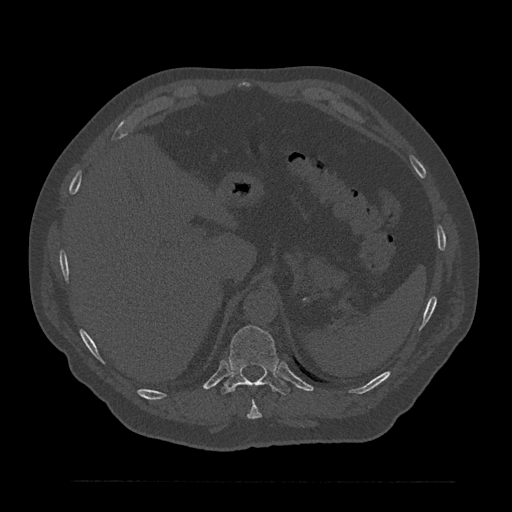
CT including the spine, one axial slice; position 308 of 797 along the scan axis; reconstruction kernel Br40s/3; 120 kVp; bone window (W 1800 / L 400 HU); 0.5 mm slice thickness; 512 × 512 image matrix, field of view 430 × 430 mm. Male patient, age 61 years. From the clinical record (not read from this slice): primary cancer: prostate.
Structures marked on this image (semi-automatic segmentation, software-assisted and operator-edited):
- T10 vertebra: bounding box (x1, y1, x2, y2) in pixels: (247, 402, 262, 419)
- T11 vertebra: (221, 325, 289, 395)